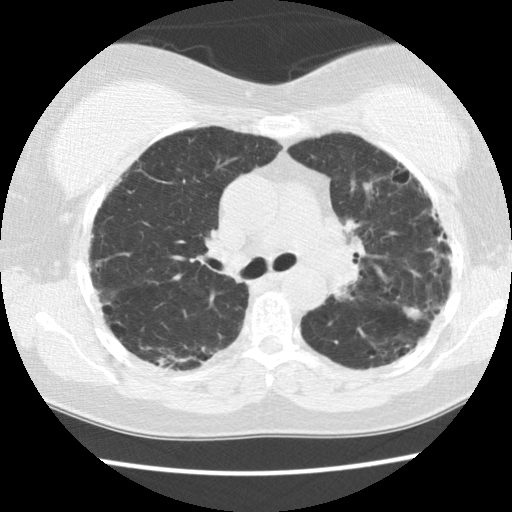
Low-dose screening chest CT, one axial slice. Reconstruction kernel STANDARD. 120 kVp. Lung window (W 1500 / L -600 HU). 2.5 mm slice thickness. 512 × 512 image matrix, field of view 320 × 320 mm.
Outlined on this slice (manually delineated by an expert):
- lesion 1 (tumor): box from (x=405, y=308) to (x=420, y=318) px